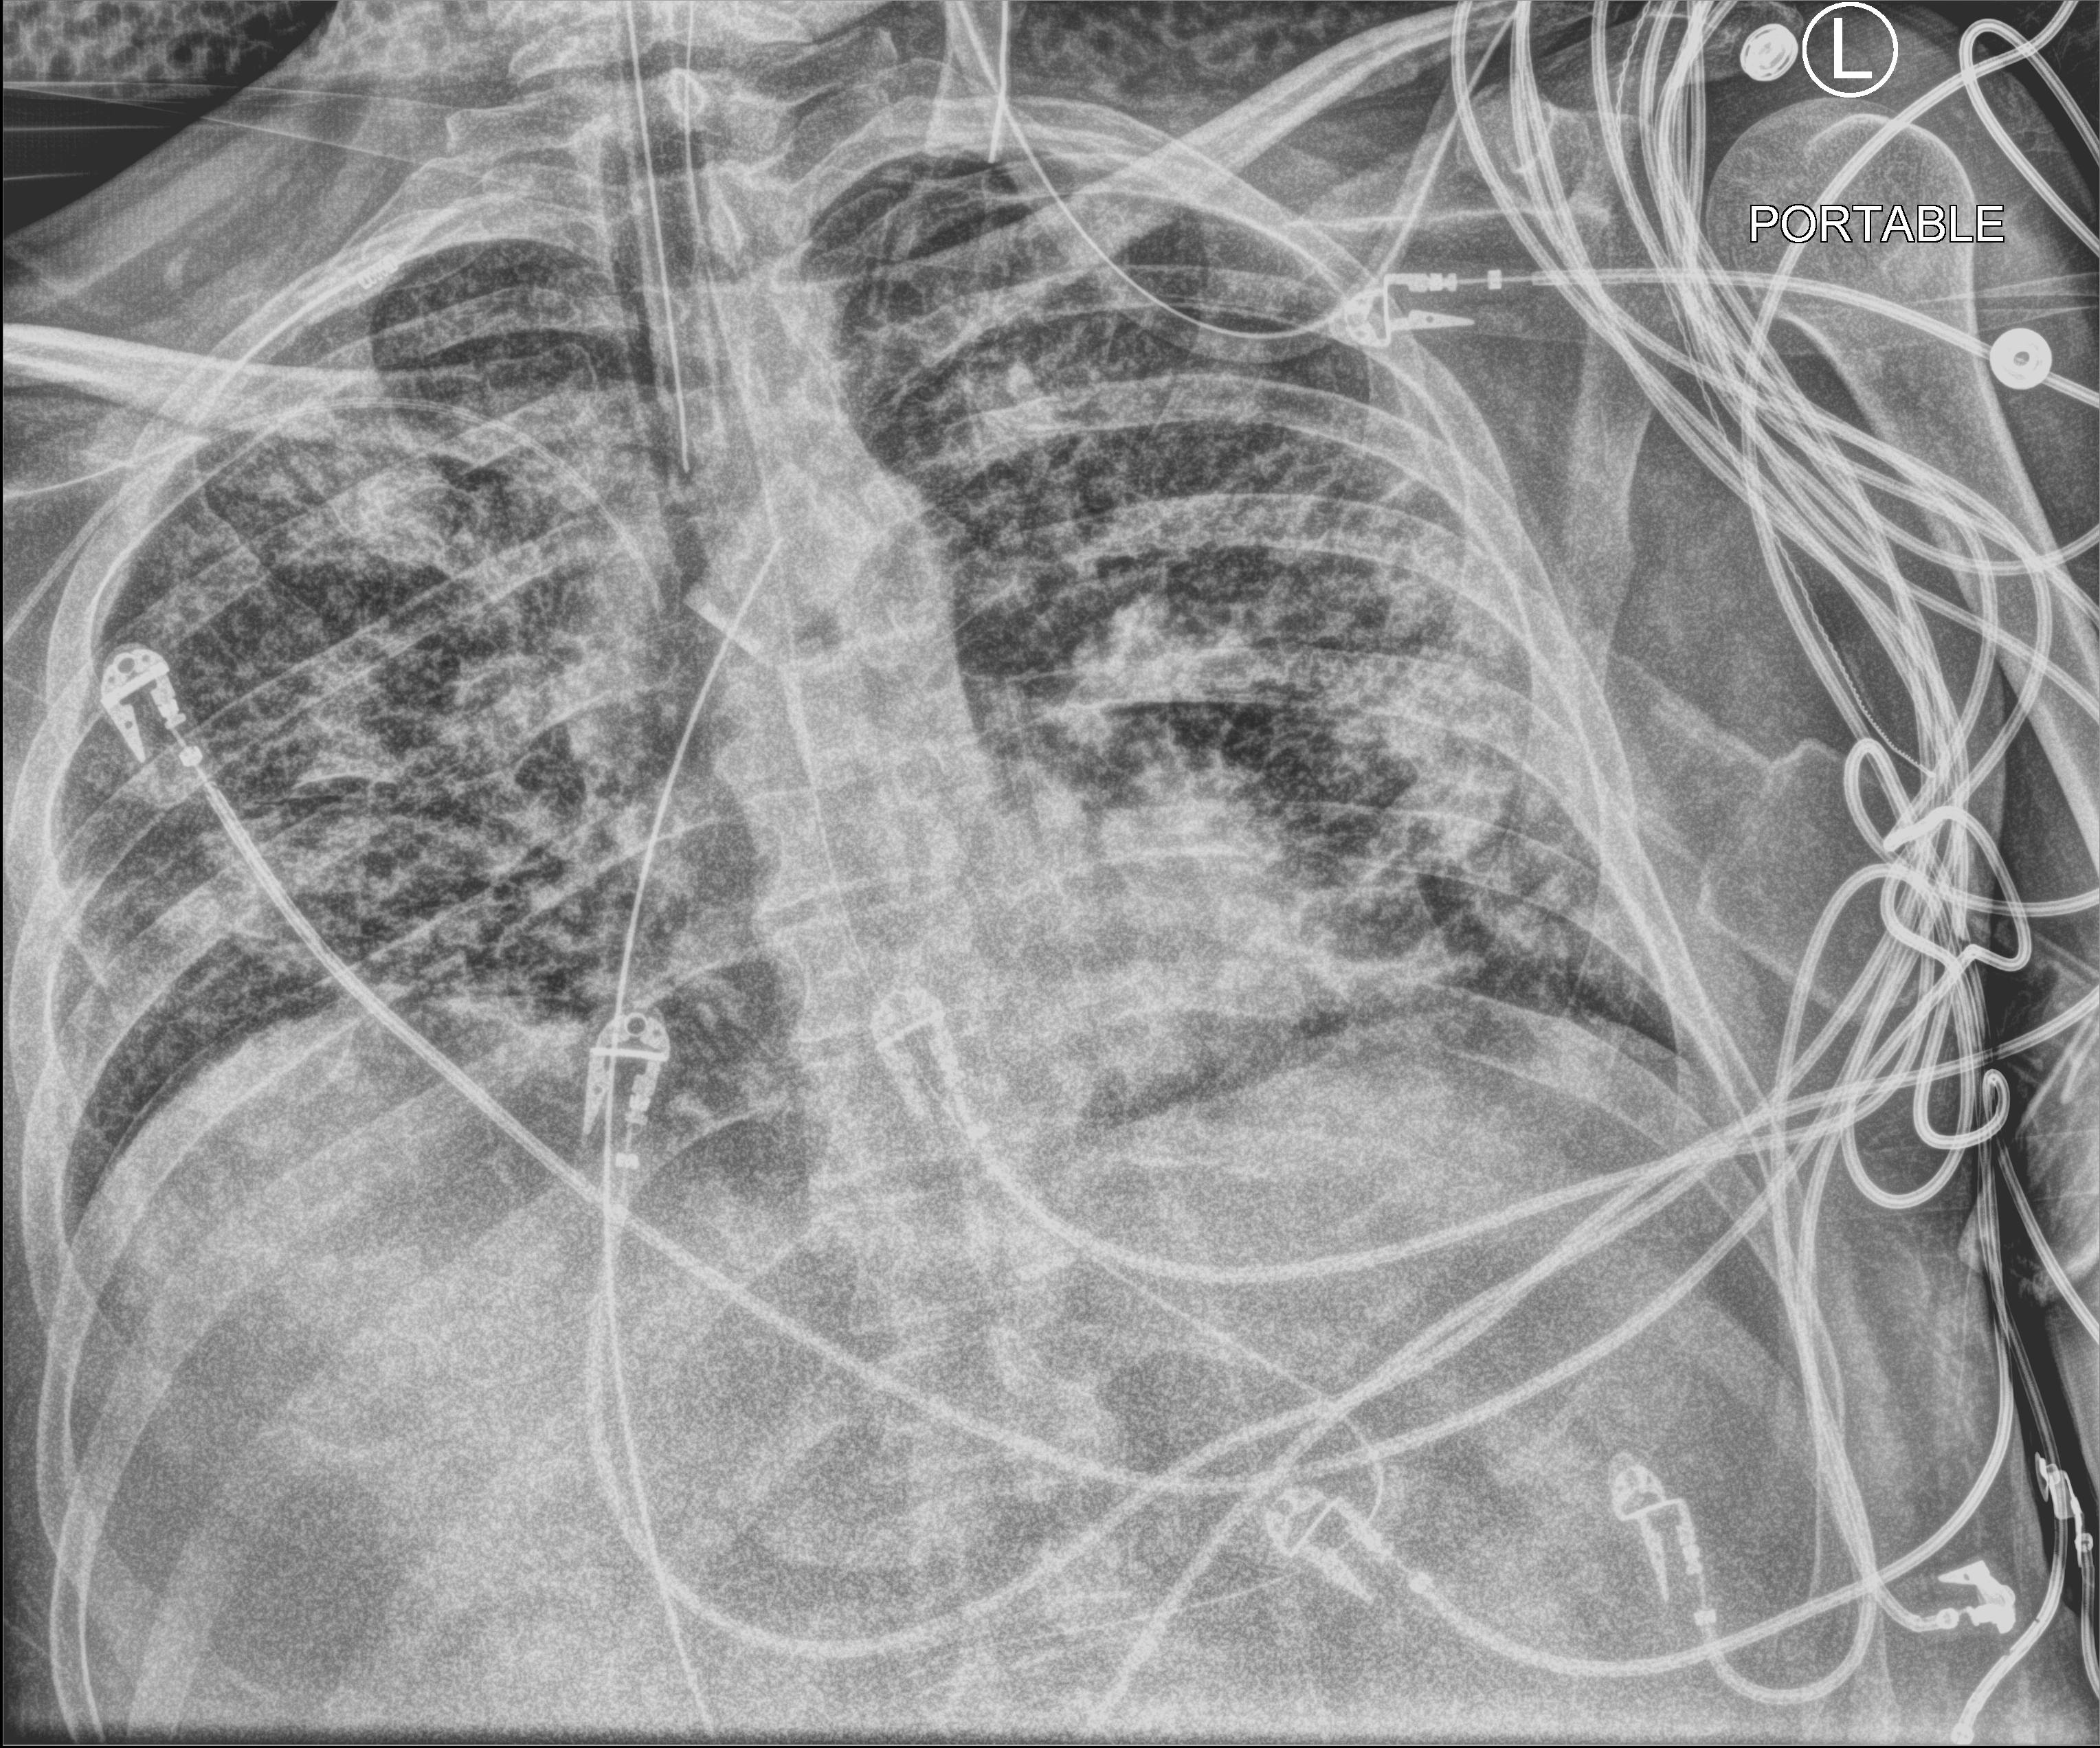
Portable chest radiograph. Male patient hospitalised with COVID-19, age 18–59 years.
From the hospital-stay record, not from the radiograph (when in the stay this image was taken is not recorded): hypertension (admission record): no; length of hospital stay: 48 days; mechanically ventilated during this hospital stay: yes.